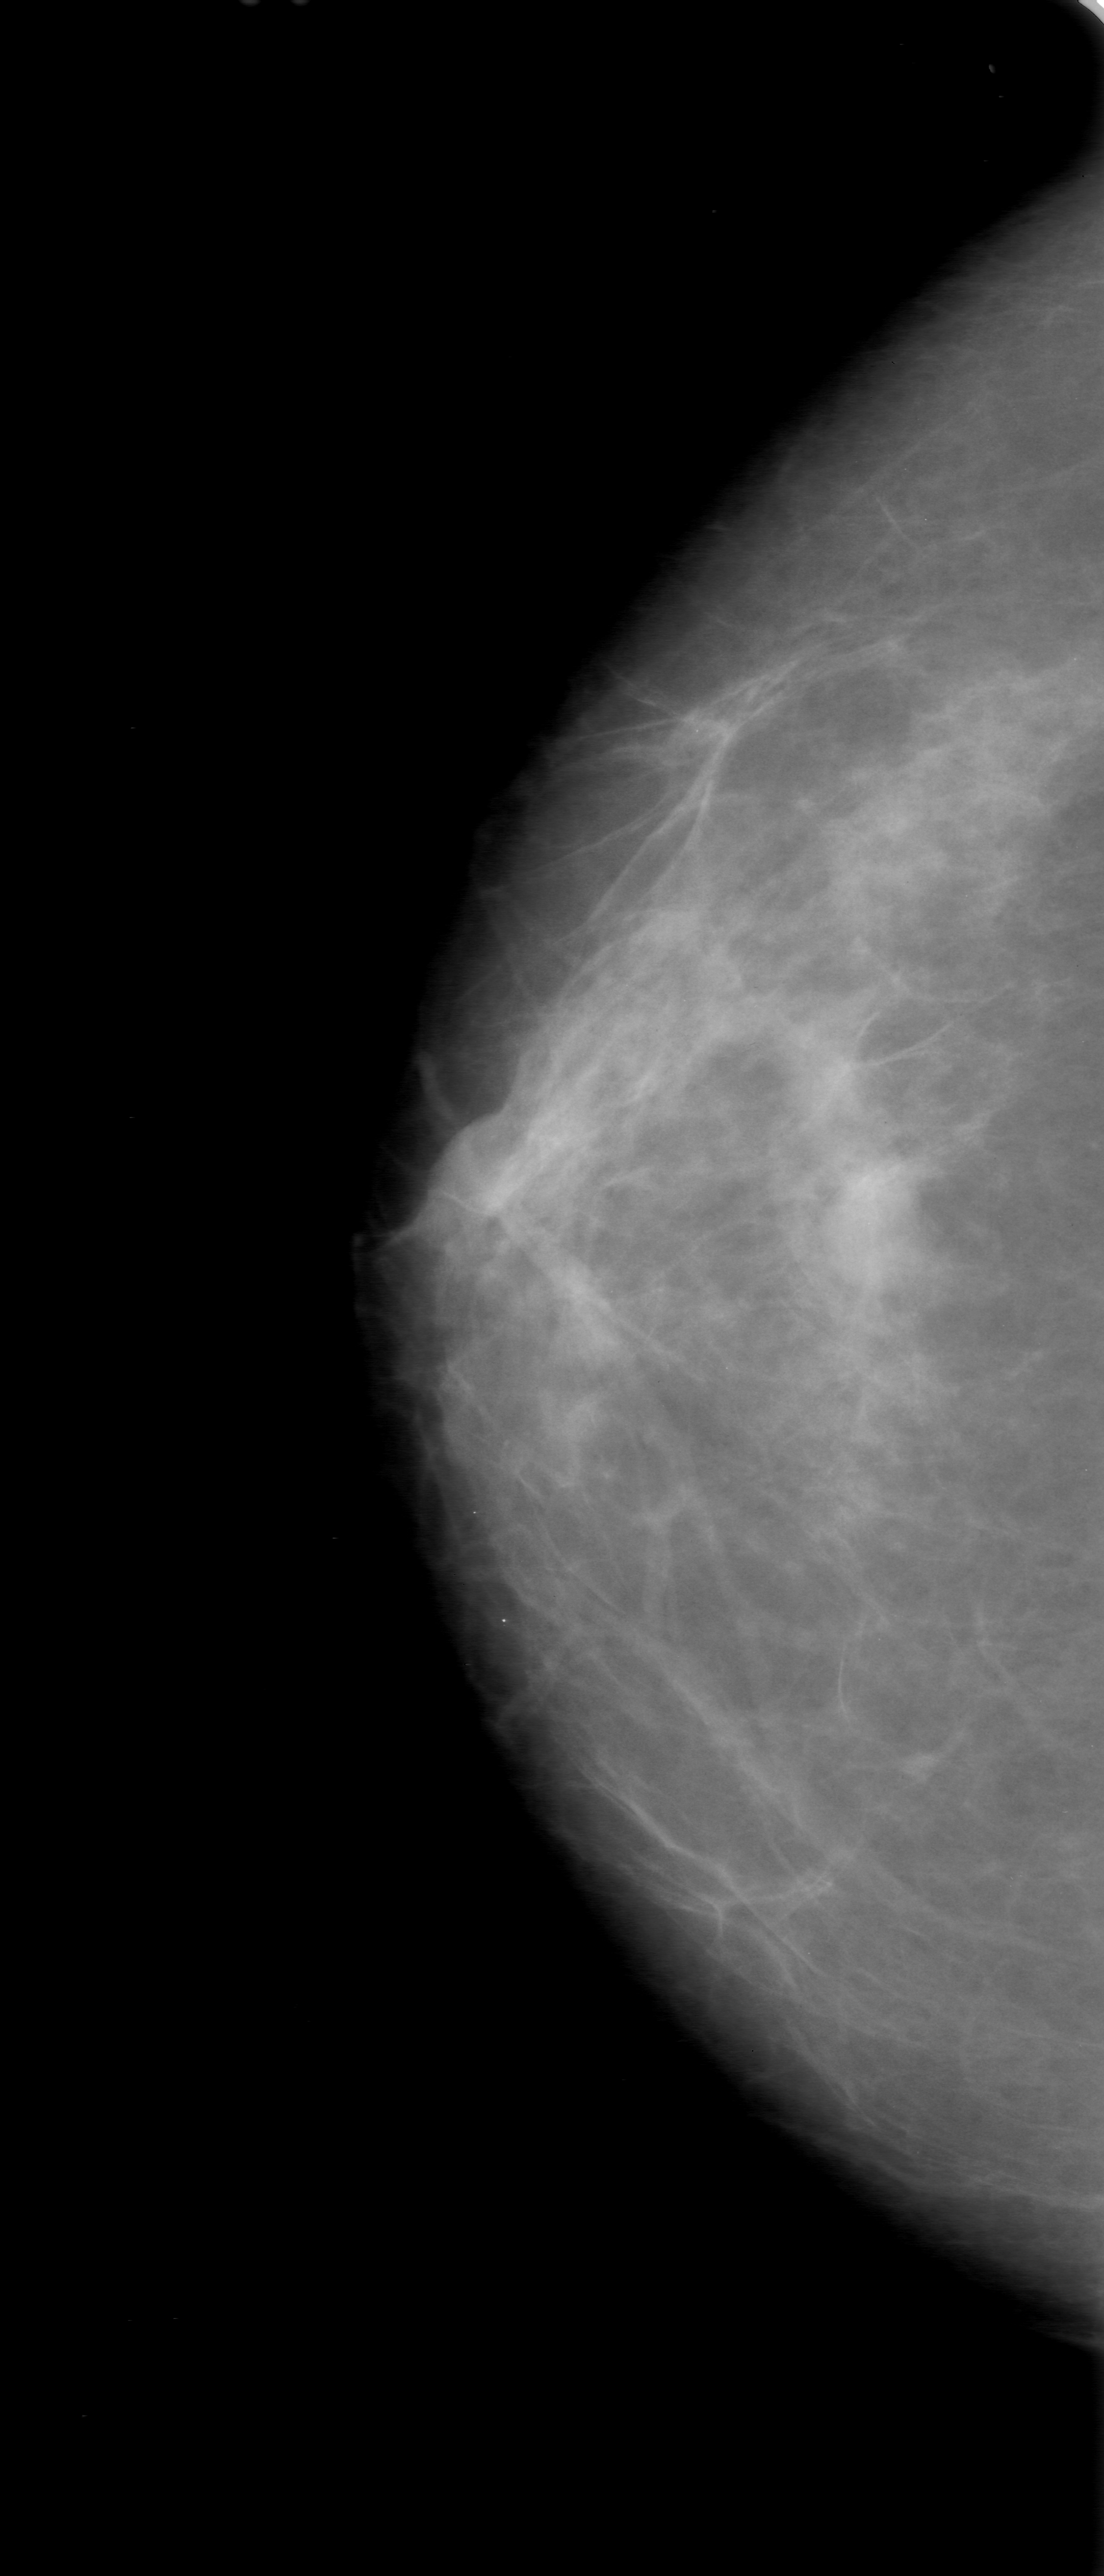
Scanned film-screen mammogram; right breast; craniocaudal (CC) view; breast composition: scattered fibroglandular densities (BI-RADS density category 2 of 4).
Abnormality record for this image: mass, shape oval, margins obscured; BI-RADS assessment category 0 (incomplete: needs additional imaging); subtlety rating 3 on a 1 (subtle) to 5 (obvious) scale; pathology result (as recorded, not read from the image): benign.